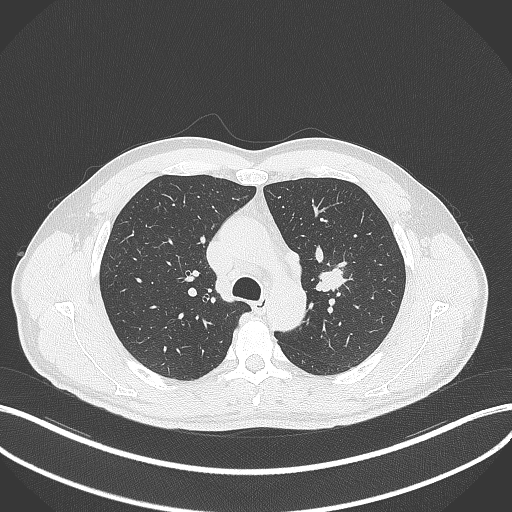
Chest CT, one axial slice. Position 296 of 392 along the scan axis. Reconstruction kernel B70f. 120 kVp. Lung window (W 1500 / L -600 HU). 1 mm slice thickness. 512 × 512 image matrix, field of view 400 × 400 mm. Male patient, age 50 years. Case-level facts recorded for this patient, not image findings: clinical TNM (as recorded): T1c N1 M1b.
Annotated regions visible in this slice (bounding box drawn by a radiologist):
- lung tumour (recorded histology: squamous cell carcinoma): bounding box (x1, y1, x2, y2) in pixels: (316, 265, 346, 295)